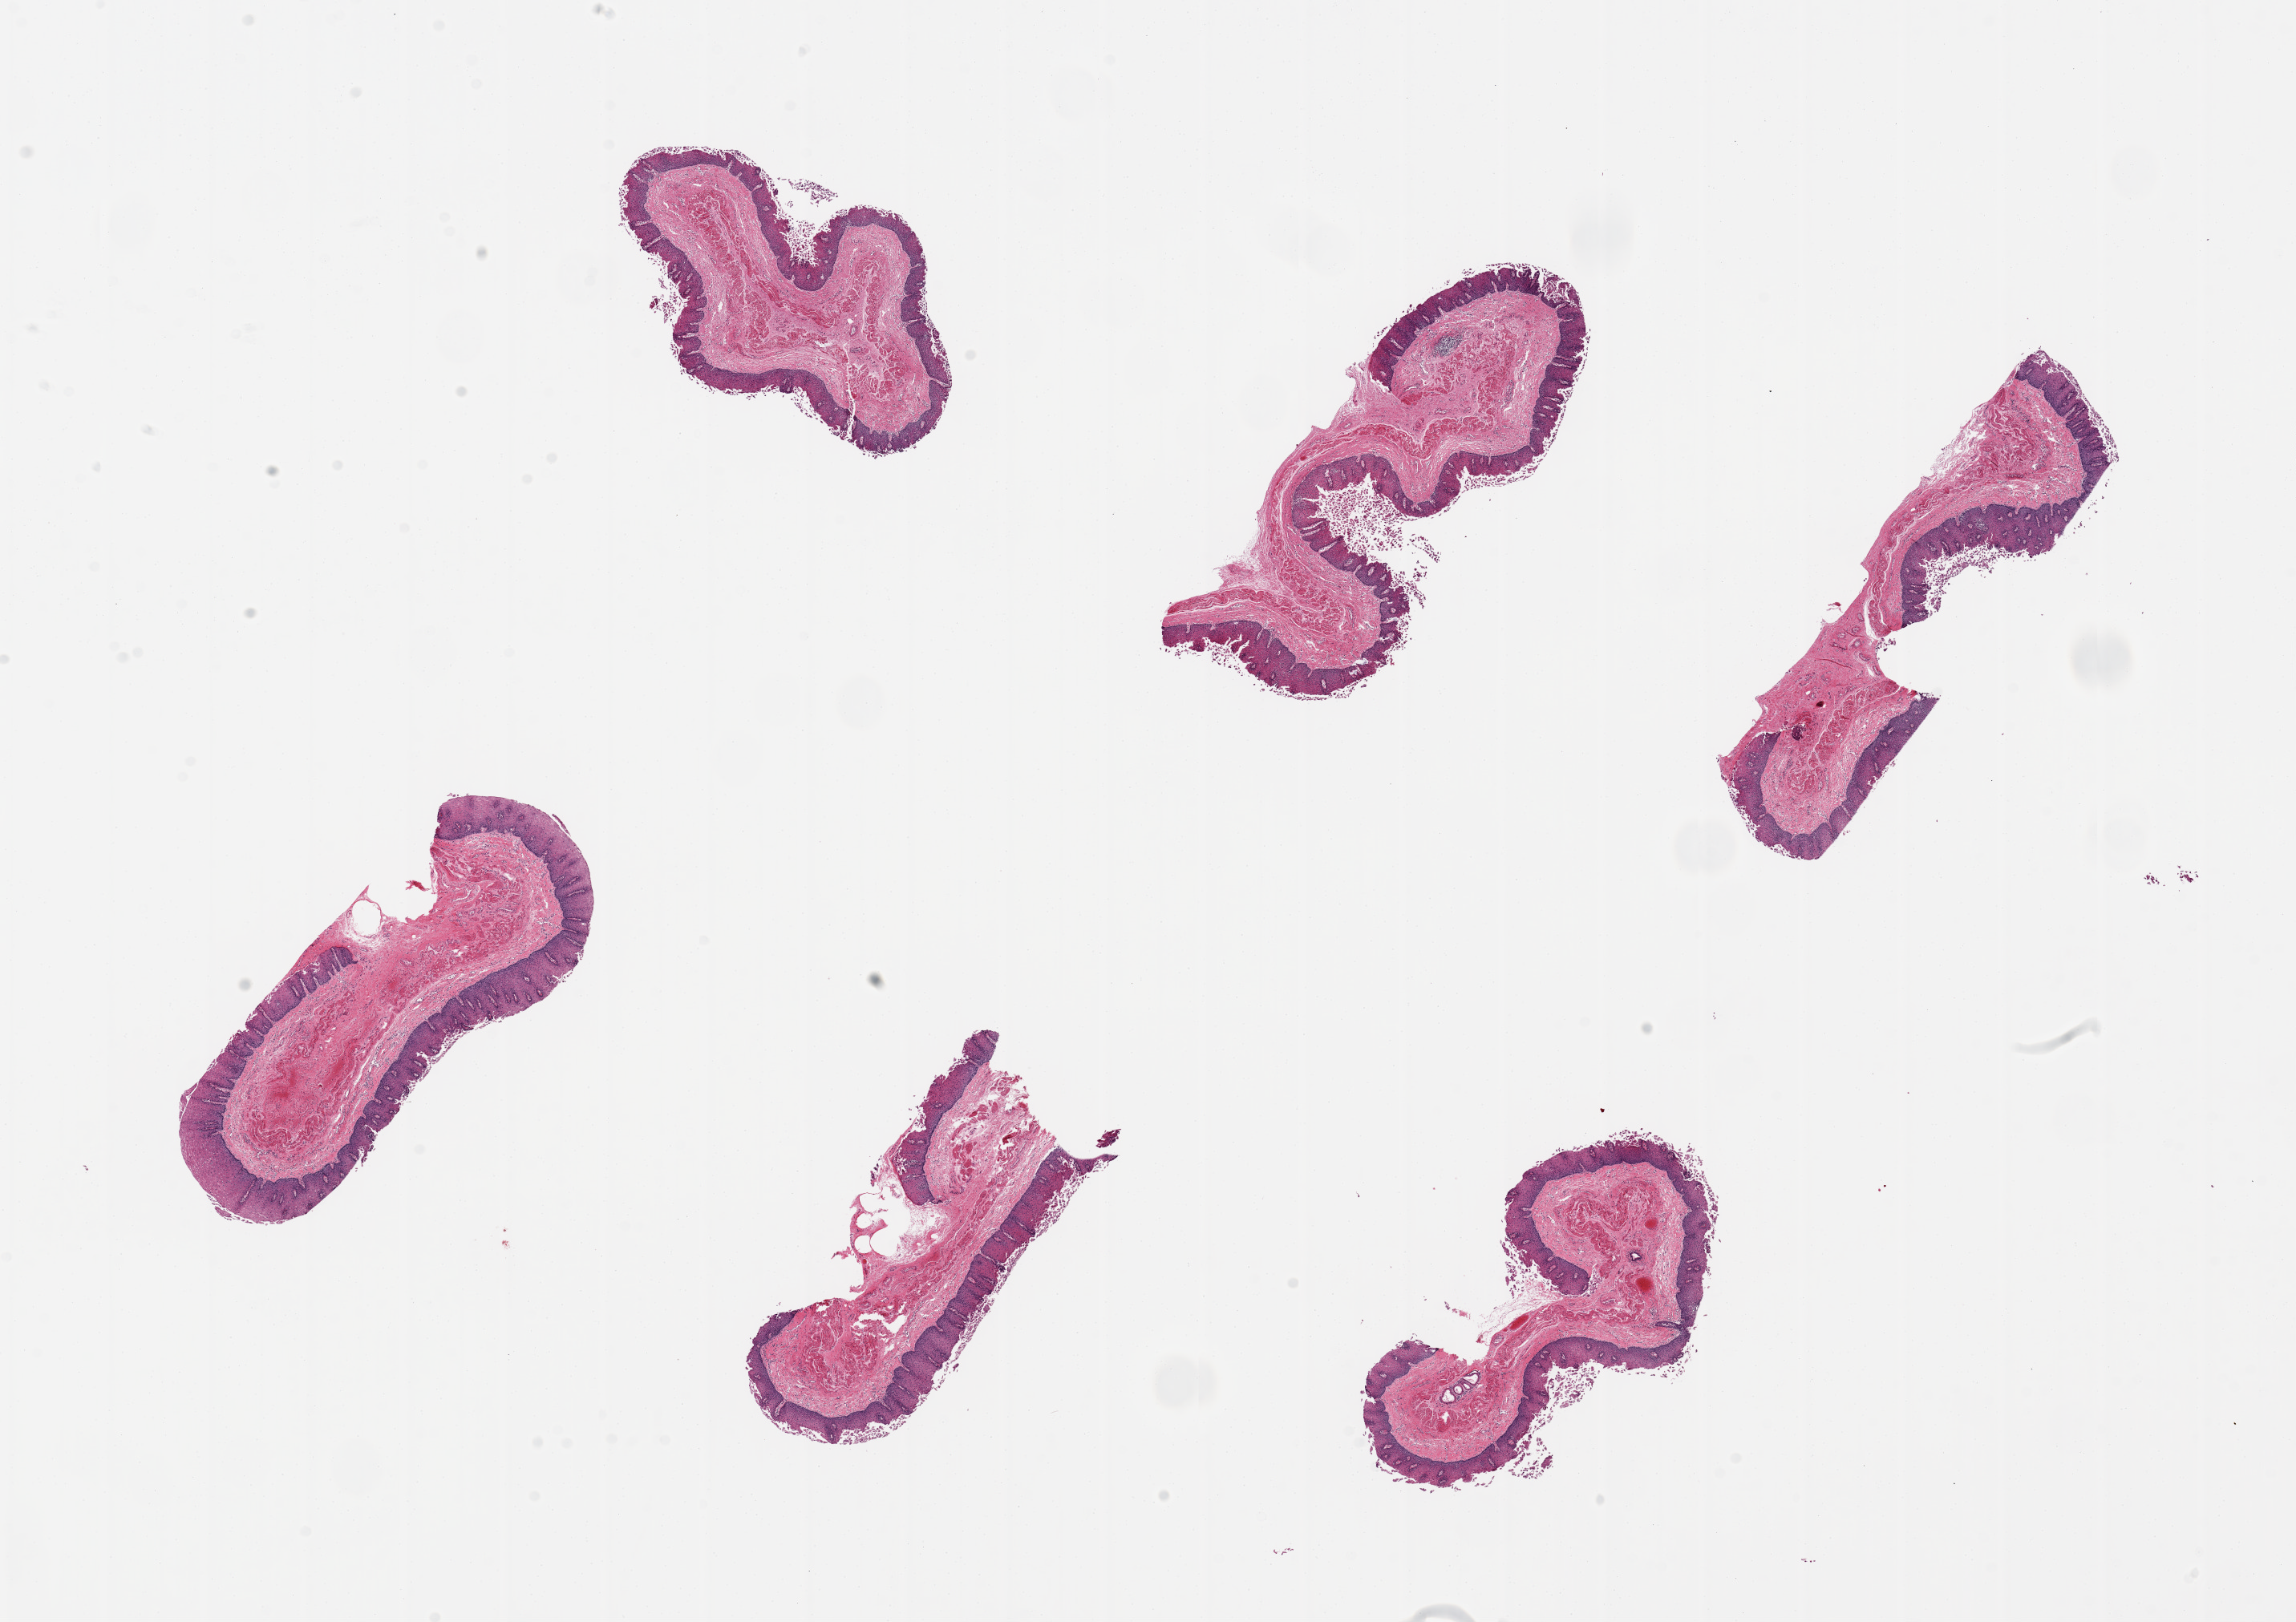
Whole-slide image, hematoxylin and eosin (H&E) stain, a low-resolution overview of the entire scanned area, about 22.6 x 16.0 mm (slide scanned at 20x); PAXgene-fixed, paraffin-embedded tissue; target tissue: esophageal mucous membrane; tissue donor sample. Donor: female.
- review note (as recorded): 6 pieces. up to 5.5x2mm; superficially sloughed epithelium